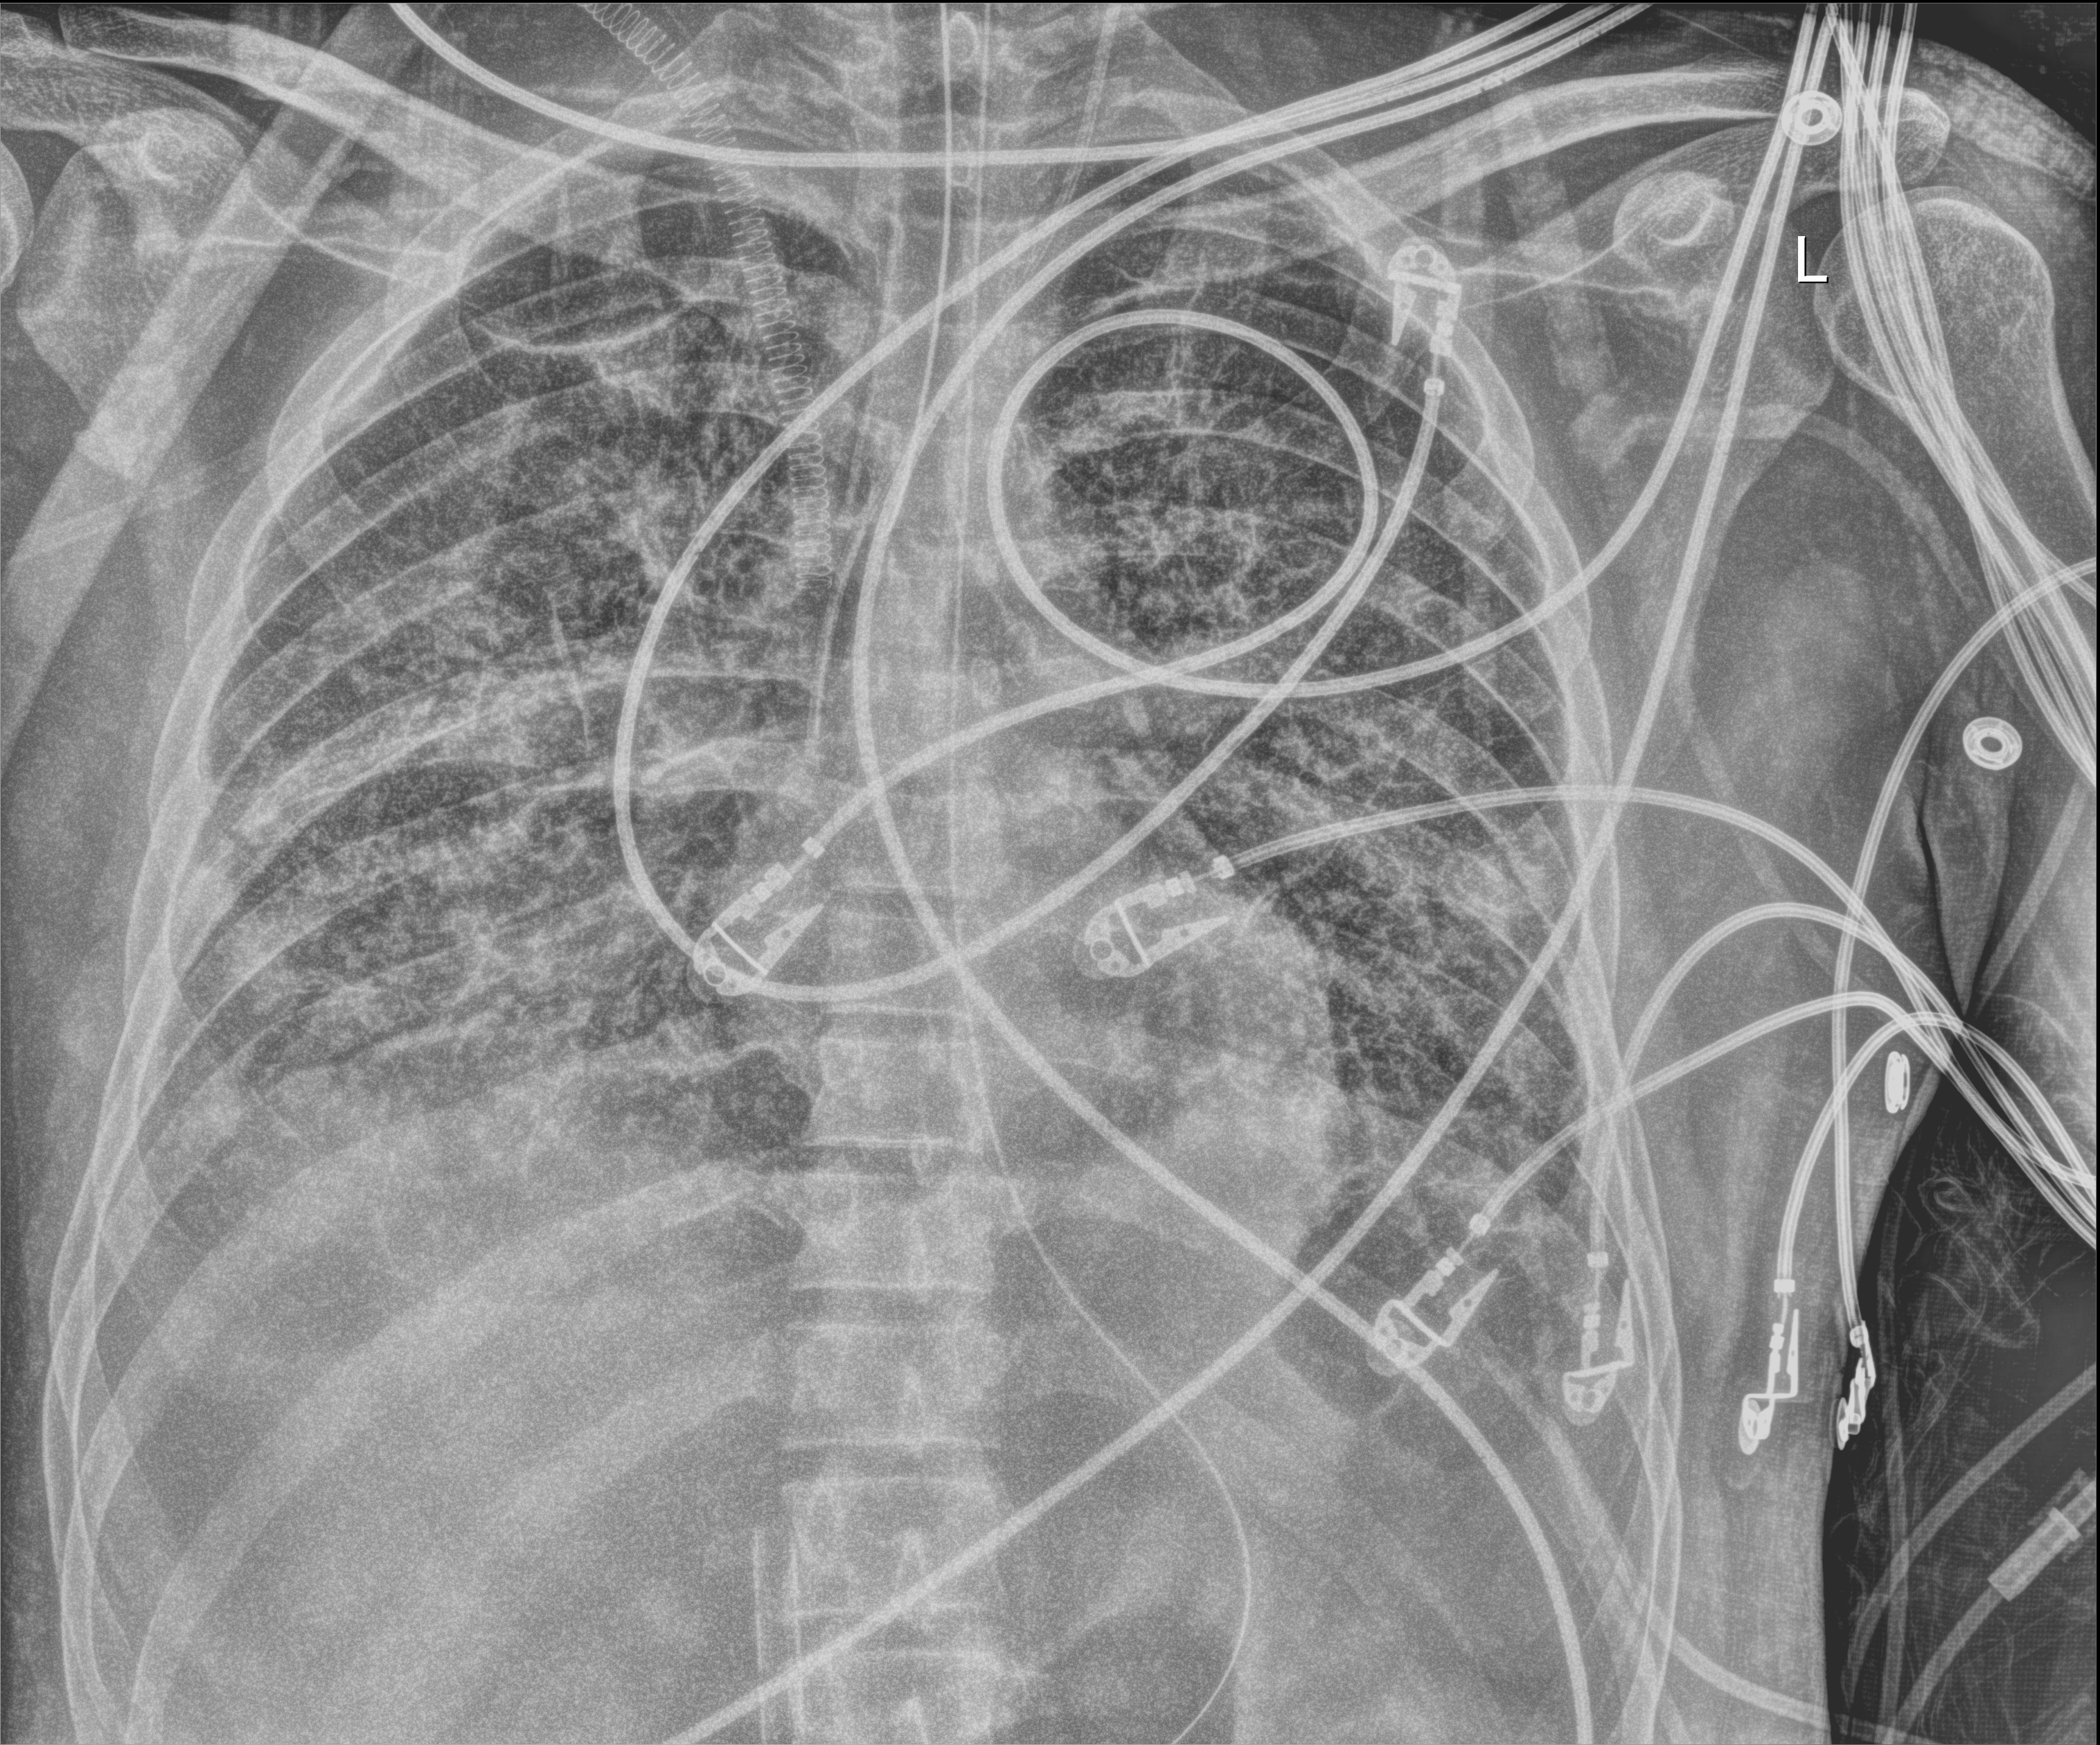
Bedside chest radiograph (digital radiography), anteroposterior (AP) projection. Patient hospitalised with COVID-19, aged 18–59 years.
From the hospital-stay record, not from the radiograph (when in the stay this image was taken is not recorded):
- diabetes (admission record): no
- admitted to intensive care during this hospital stay: yes